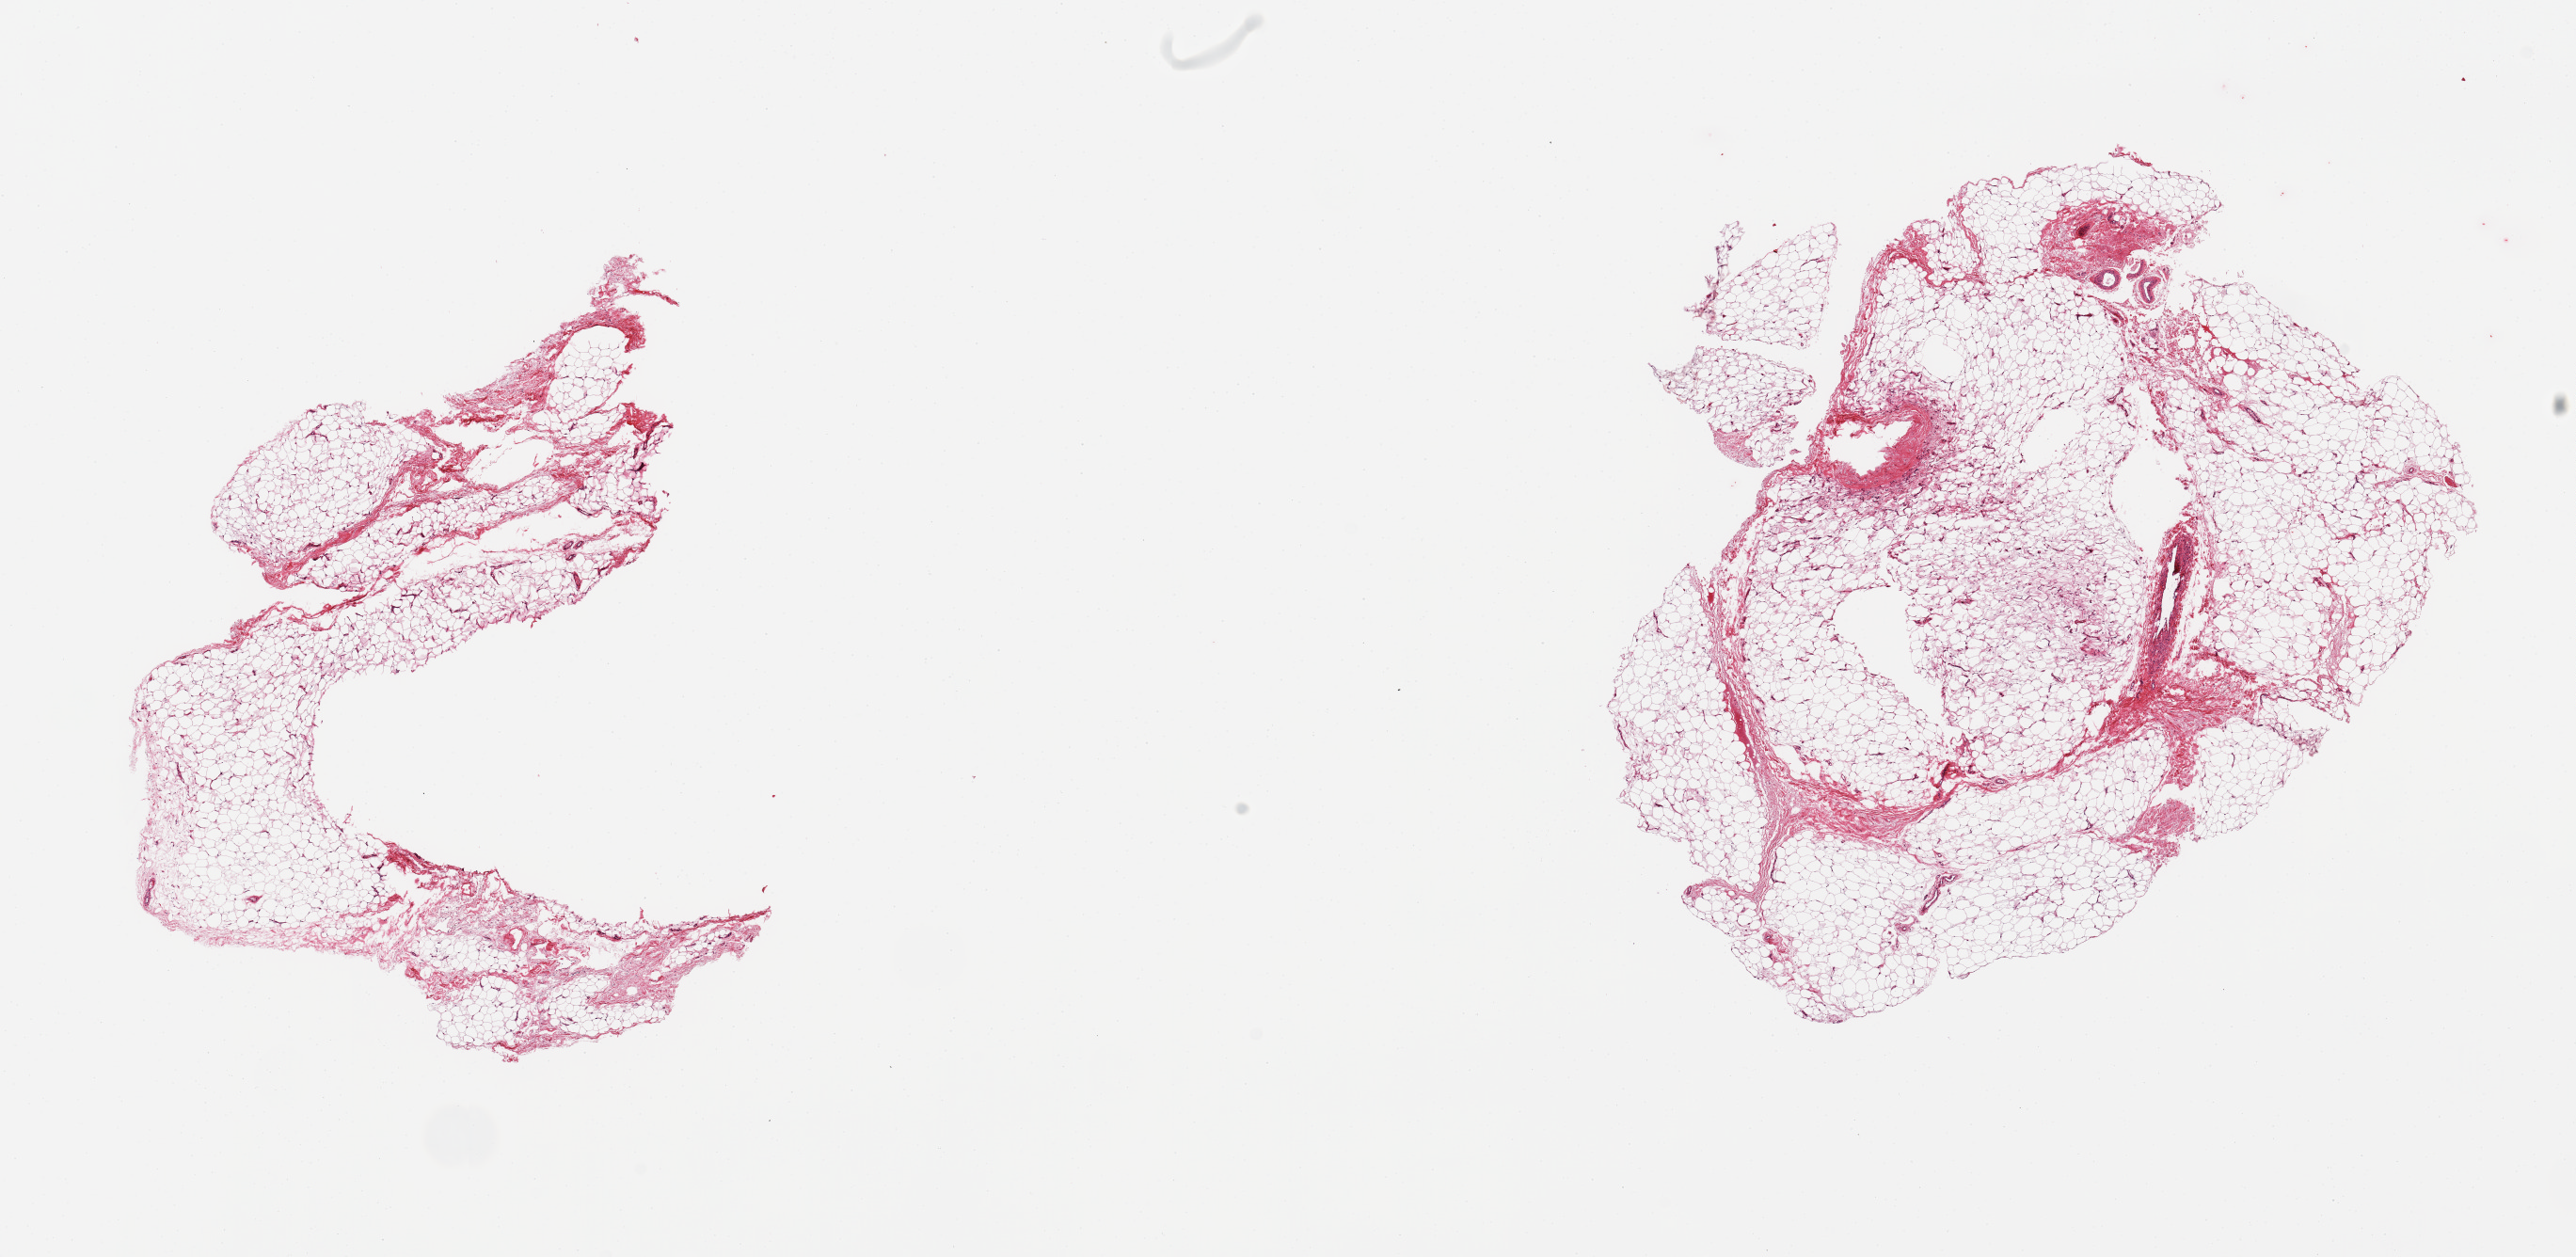
Digitized haematoxylin and eosin-stained section — a low-resolution overview of the entire scanned area, about 21.7 x 10.6 mm (from a 20x scan). PAXgene-fixed paraffin-embedded (PFPE) section. Section of adipose tissue (target tissue). Tissue donor sample. Donor sex: male.
- pathologist's review note for this sample: 2 pieces; 5 & 10% fibrovascular content